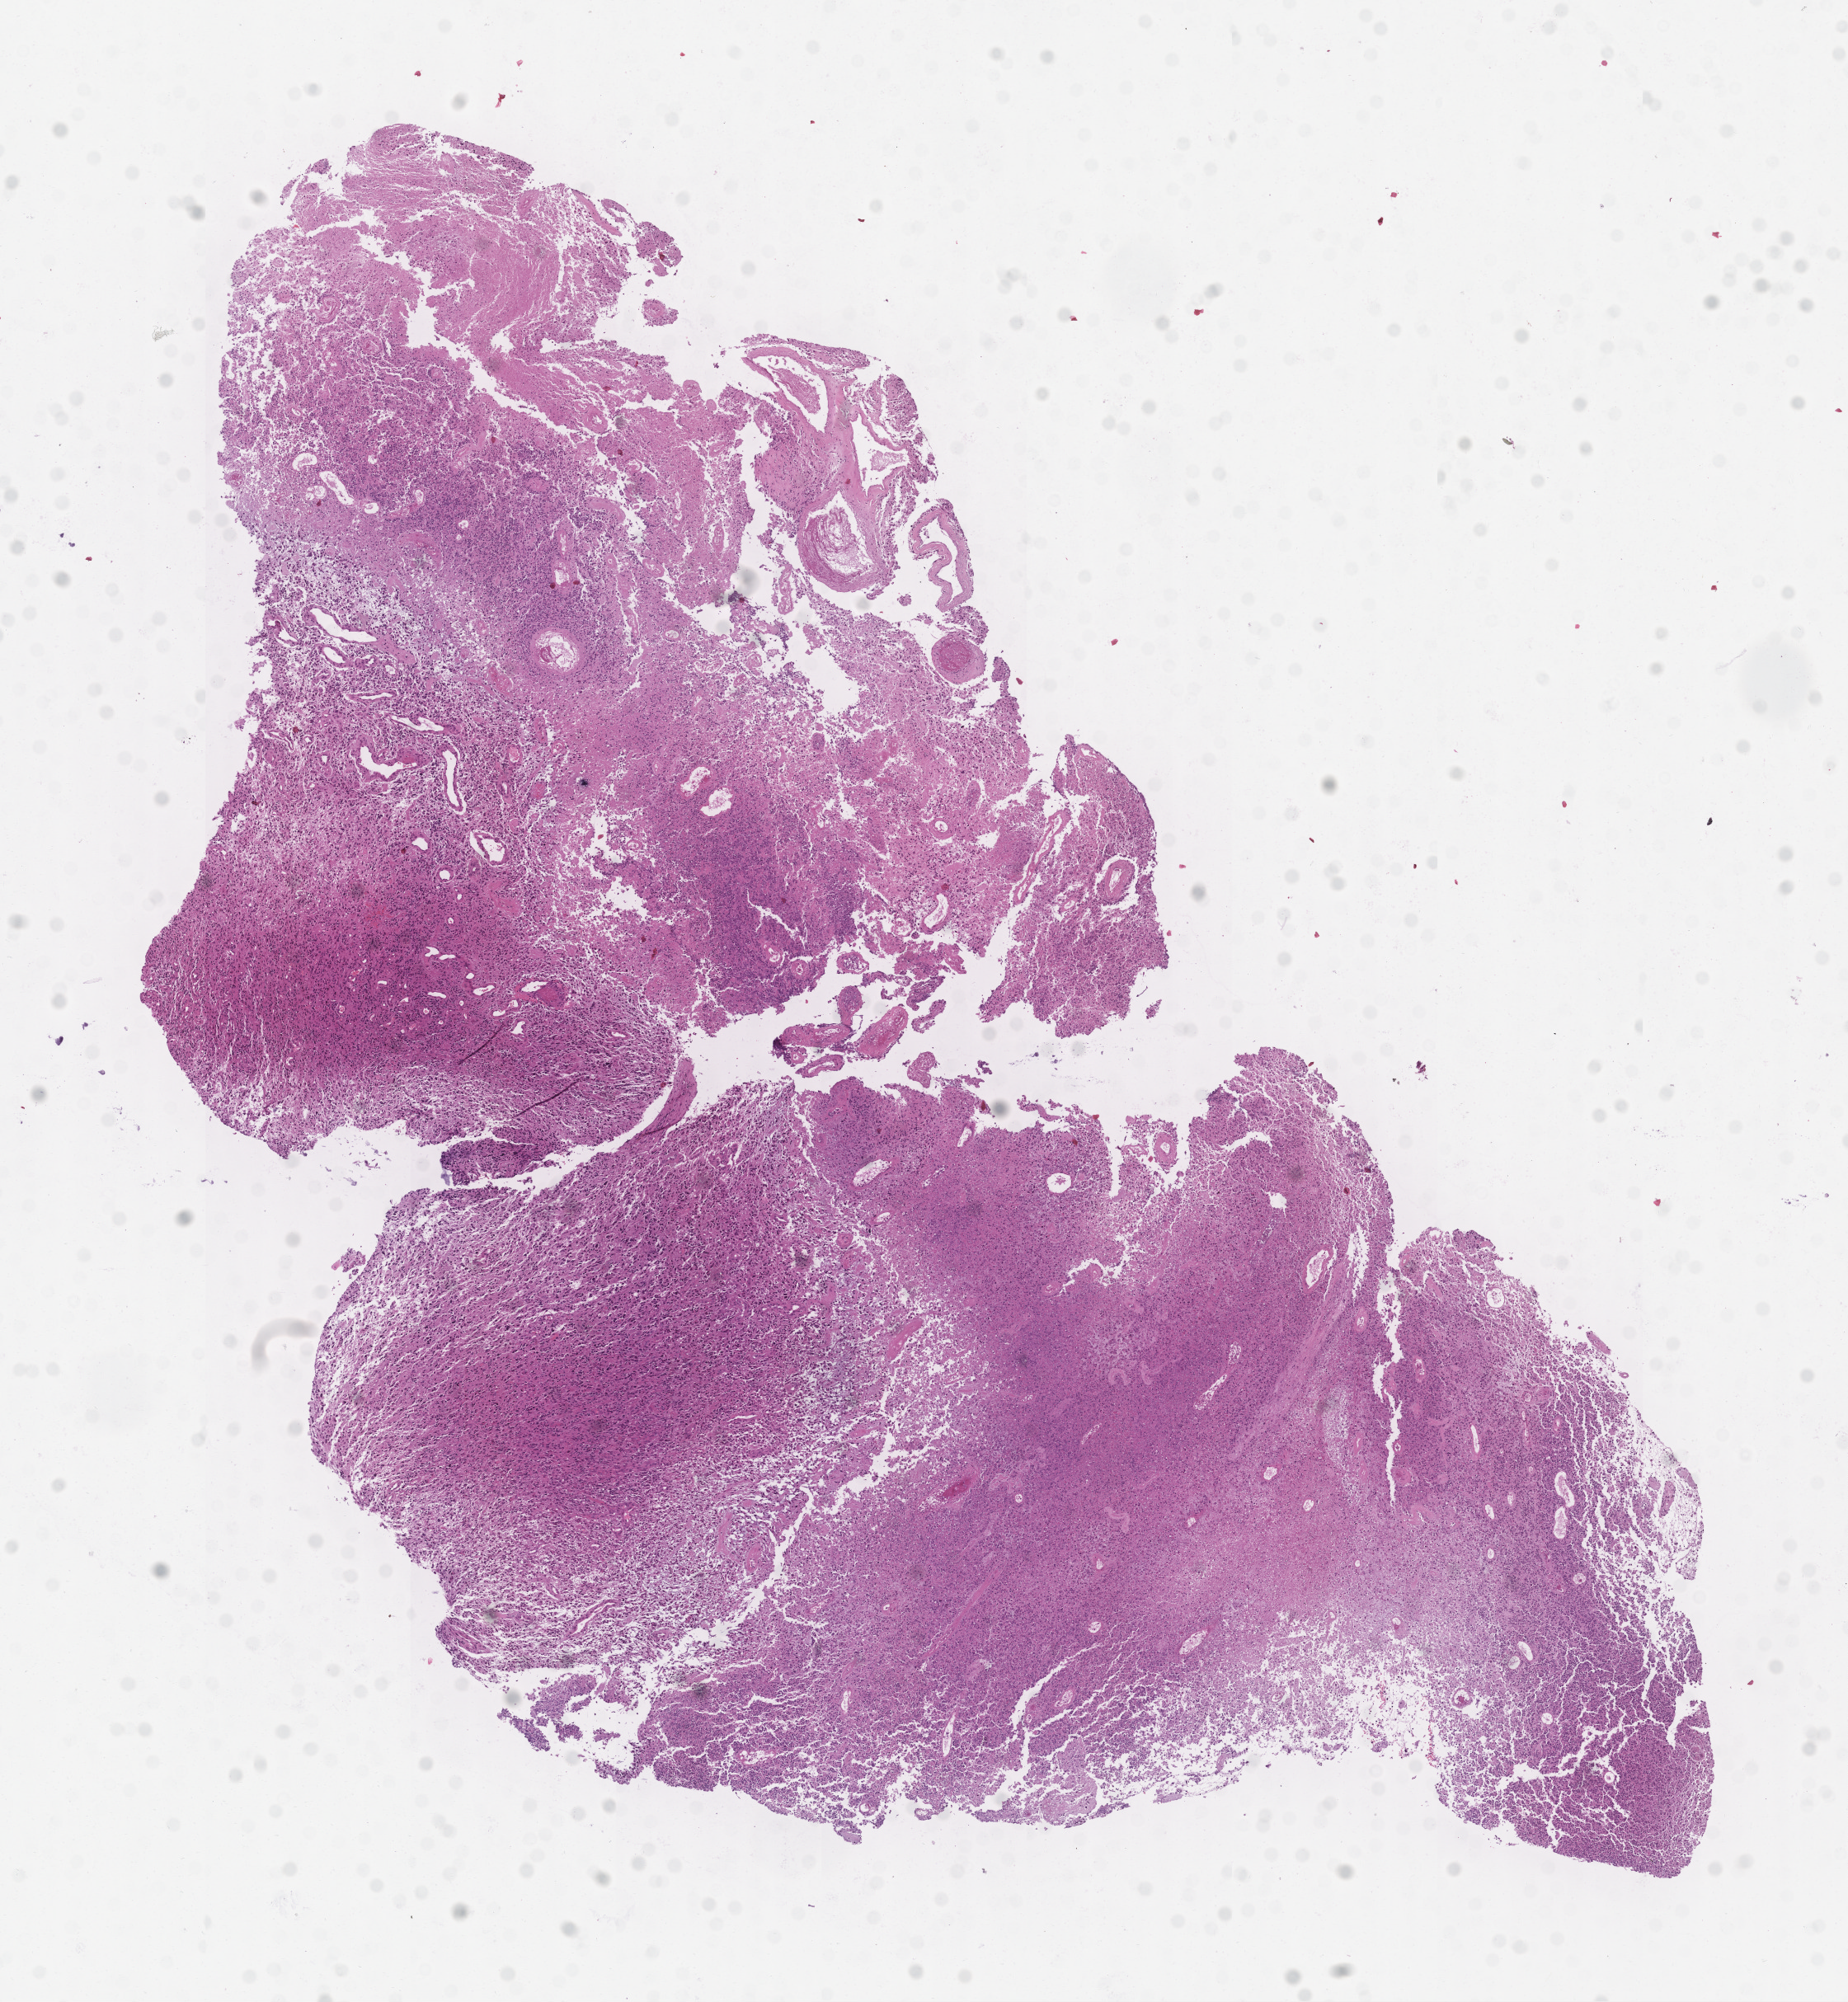
Whole-slide histology image, H&E-stained — a low-resolution overview of the entire scanned area, about 9.0 x 9.8 mm (slide scanned at 20x); tumour tissue sample, brain. Male, 62 y/o.
Diagnosis: Glioblastoma.